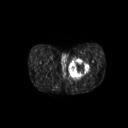
FDG PET of an extremity soft-tissue mass (from a PET/CT study), one axial slice. Position 33 of 267 along the scan axis. 3.27 mm slice thickness. 128 × 128 image matrix, field of view 600 × 600 mm. Patient: male, 59 years. From the clinical record (not read from this slice): histological type: pleiomorphic liposarcoma; grade: high; site of the primary tumour: left thigh.
Structures marked on this image (expert contour drawn on MRI and transferred to this co-registered scan by the dataset authors):
- gross tumour volume including surrounding oedema: bounding box <69,58,89,79> (left, top, right, bottom; pixels)
- gross tumour volume (mass): <69,58,89,77>